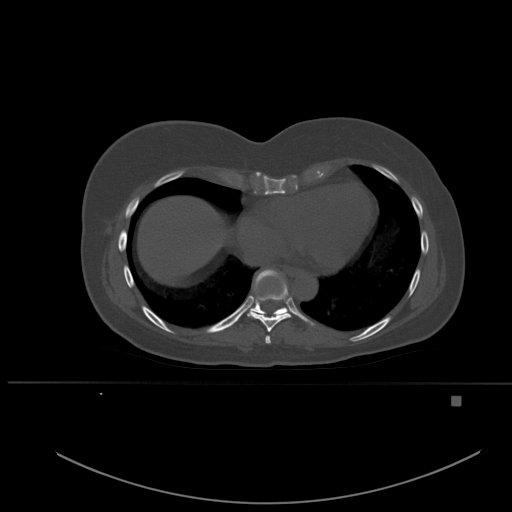
CT including the spine, one axial slice; slice 315 of 651 in the series (ordered by position); bone window (W 1800 / L 400 HU); 1.5 mm slice thickness; 512 × 512 image matrix, field of view 443 × 443 mm. Female patient, age 49 years. From the clinical record (not read from this slice): primary cancer: breast; vertebrae with lytic lesions (as recorded): L3, T12, L4.
Outlined on this slice (semi-automatically segmented with operator editing):
- T7 vertebra: bounding box <265,335,271,344> (left, top, right, bottom; pixels)
- T8 vertebra: <249,281,291,332>
- T9 vertebra: <227,269,288,320>